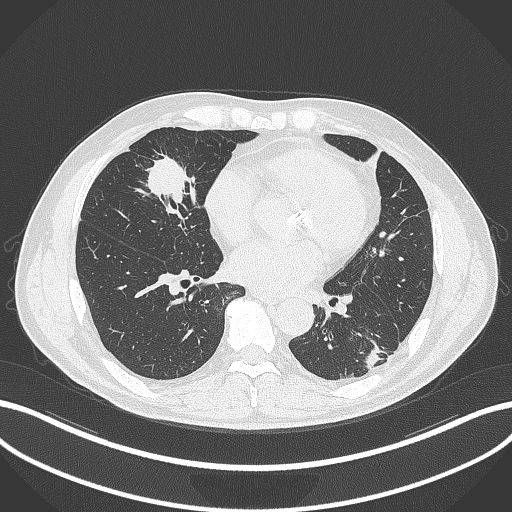
Chest CT, one axial slice; position 121 of 399 along the scan axis; reconstruction kernel B70f; 120 kVp; lung window (W 1500 / L -600 HU); 1 mm slice thickness; 512 × 512 image matrix, field of view 400 × 400 mm. Male patient, age 59 years. Case-level facts recorded for this patient, not image findings: clinical TNM (as recorded): T2a N1 M0.
Outlined on this slice (rectangle marked by the reading radiologist):
- lung tumour (recorded histology: adenocarcinoma): box from (x=137, y=150) to (x=201, y=214) px